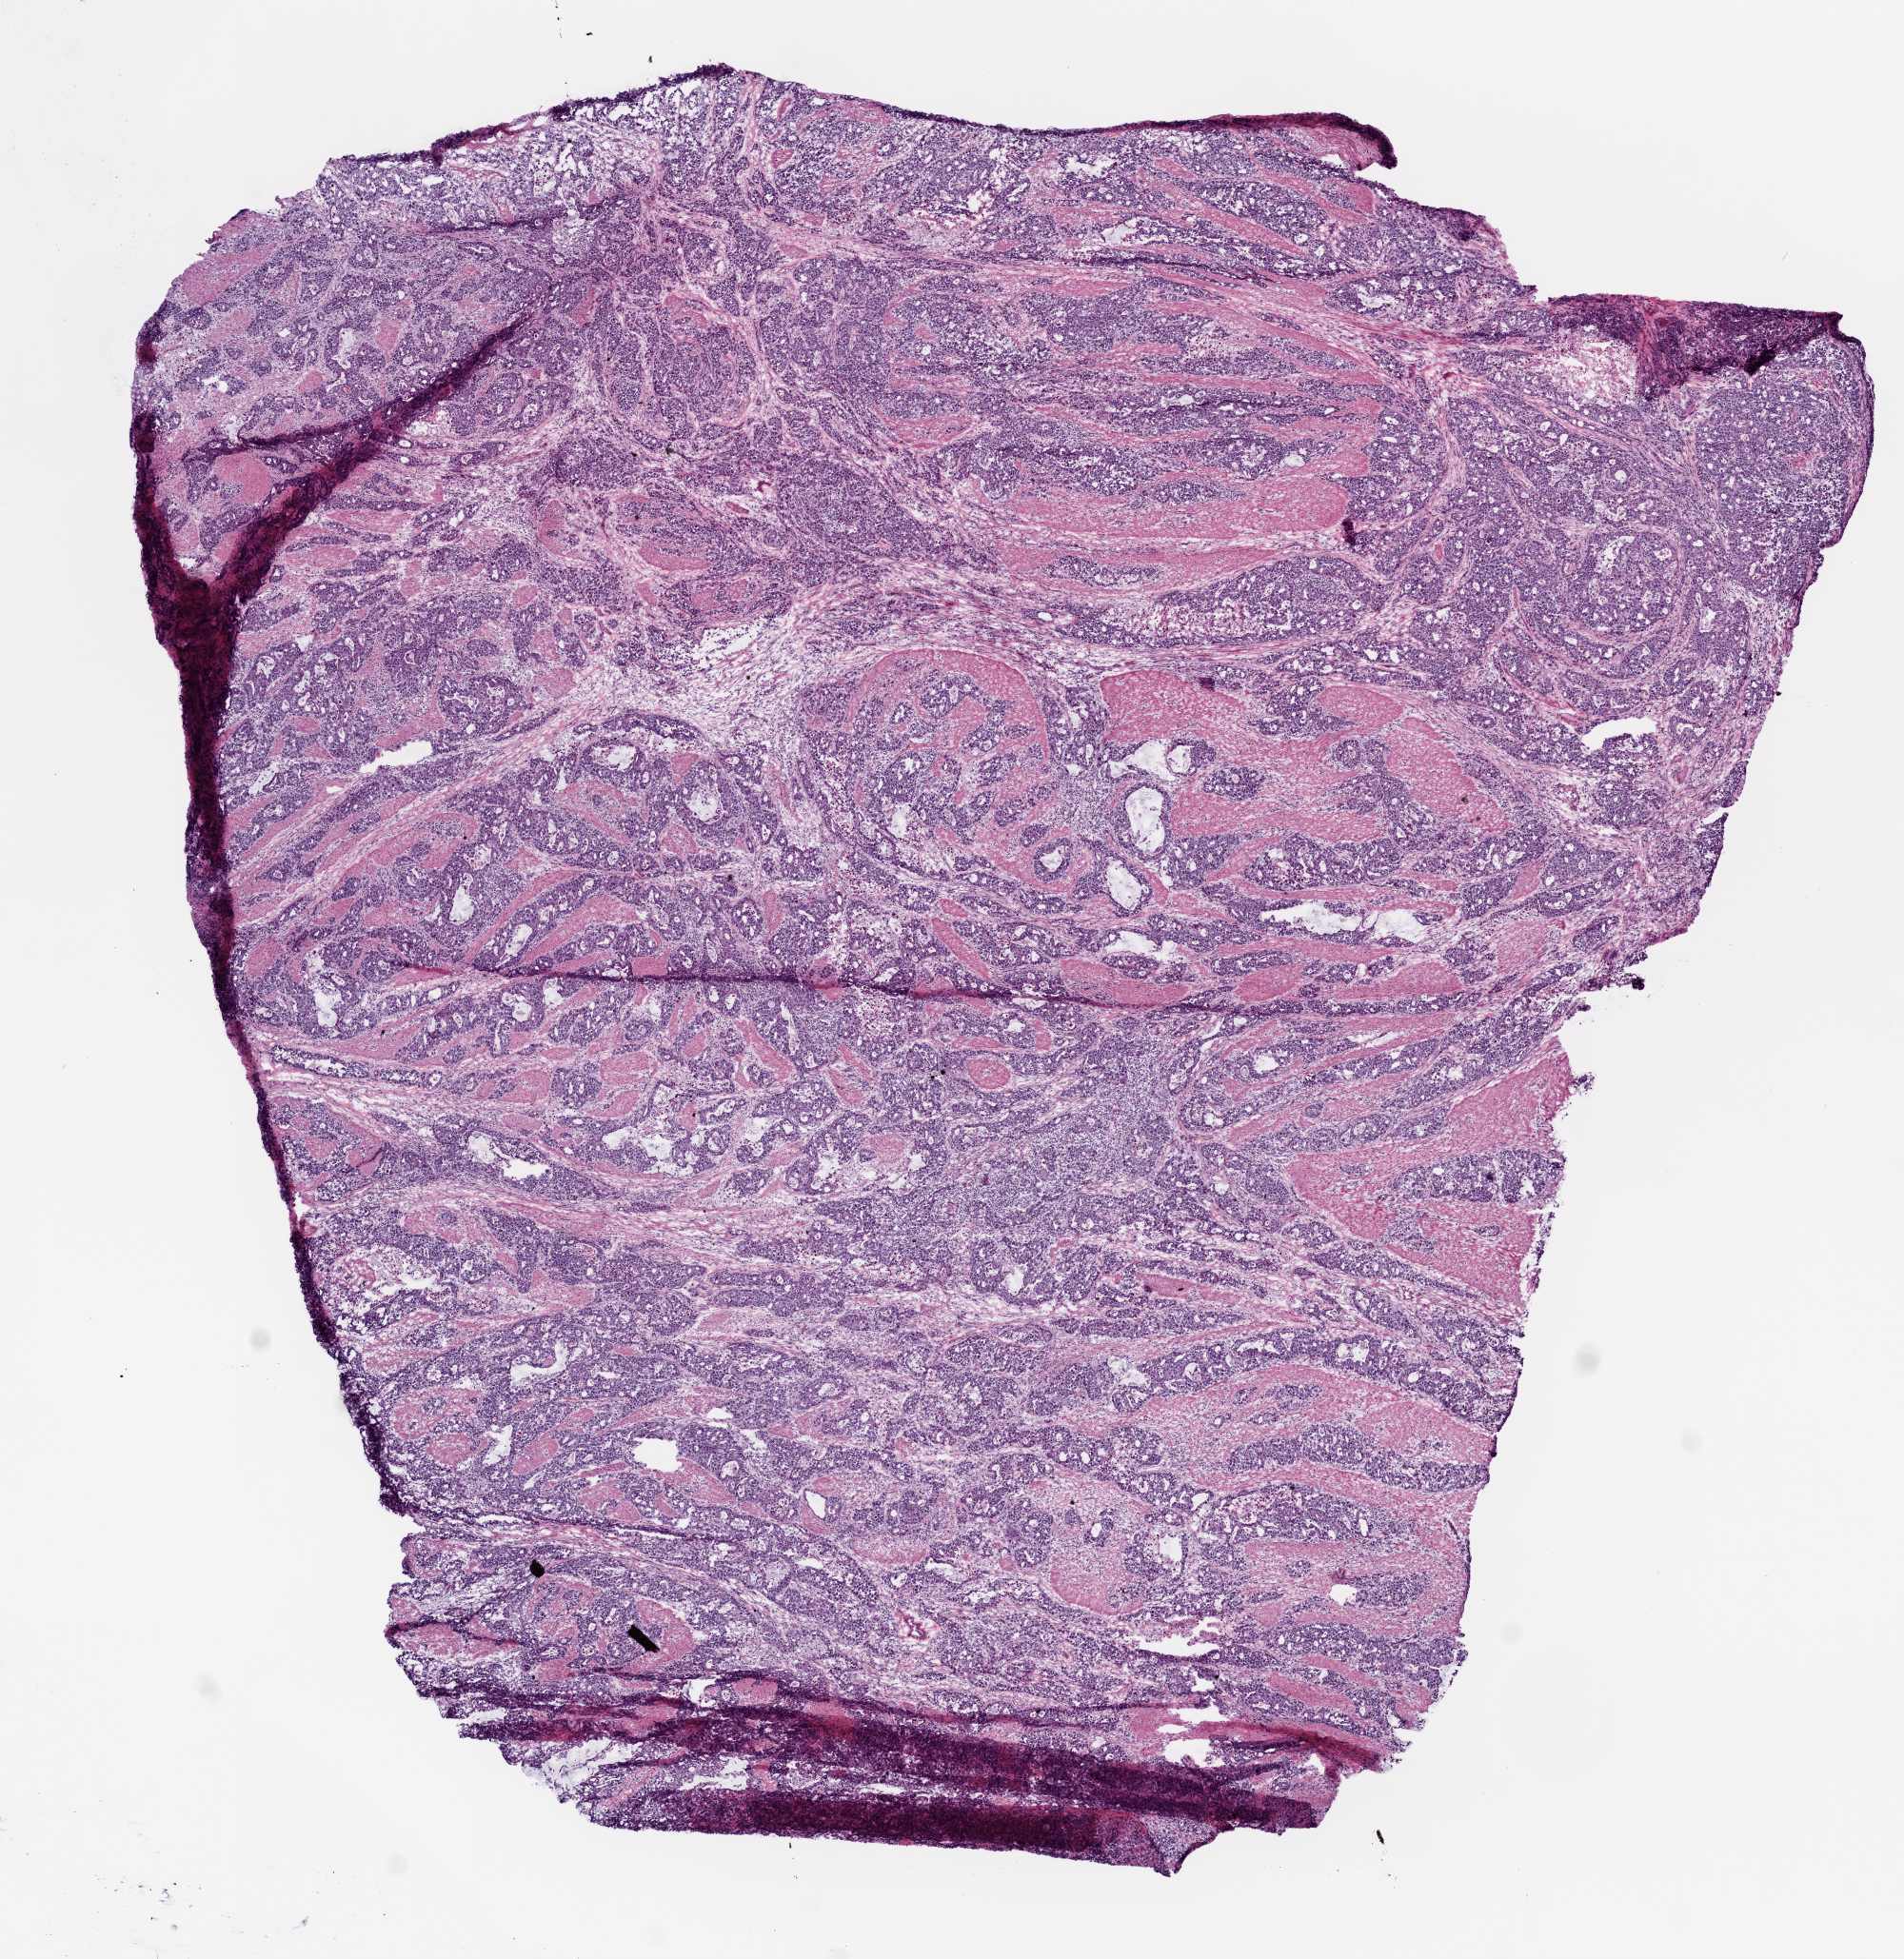
H&E-stained whole-slide image, low-resolution overview of the scanned area, about 8.0 x 8.3 mm (slide scanned at 20x). Frozen section. Primary tumour sample from the stomach. Male patient; age at initial diagnosis 56 years.
Pathologic diagnosis: Adenocarcinoma, intestinal type.